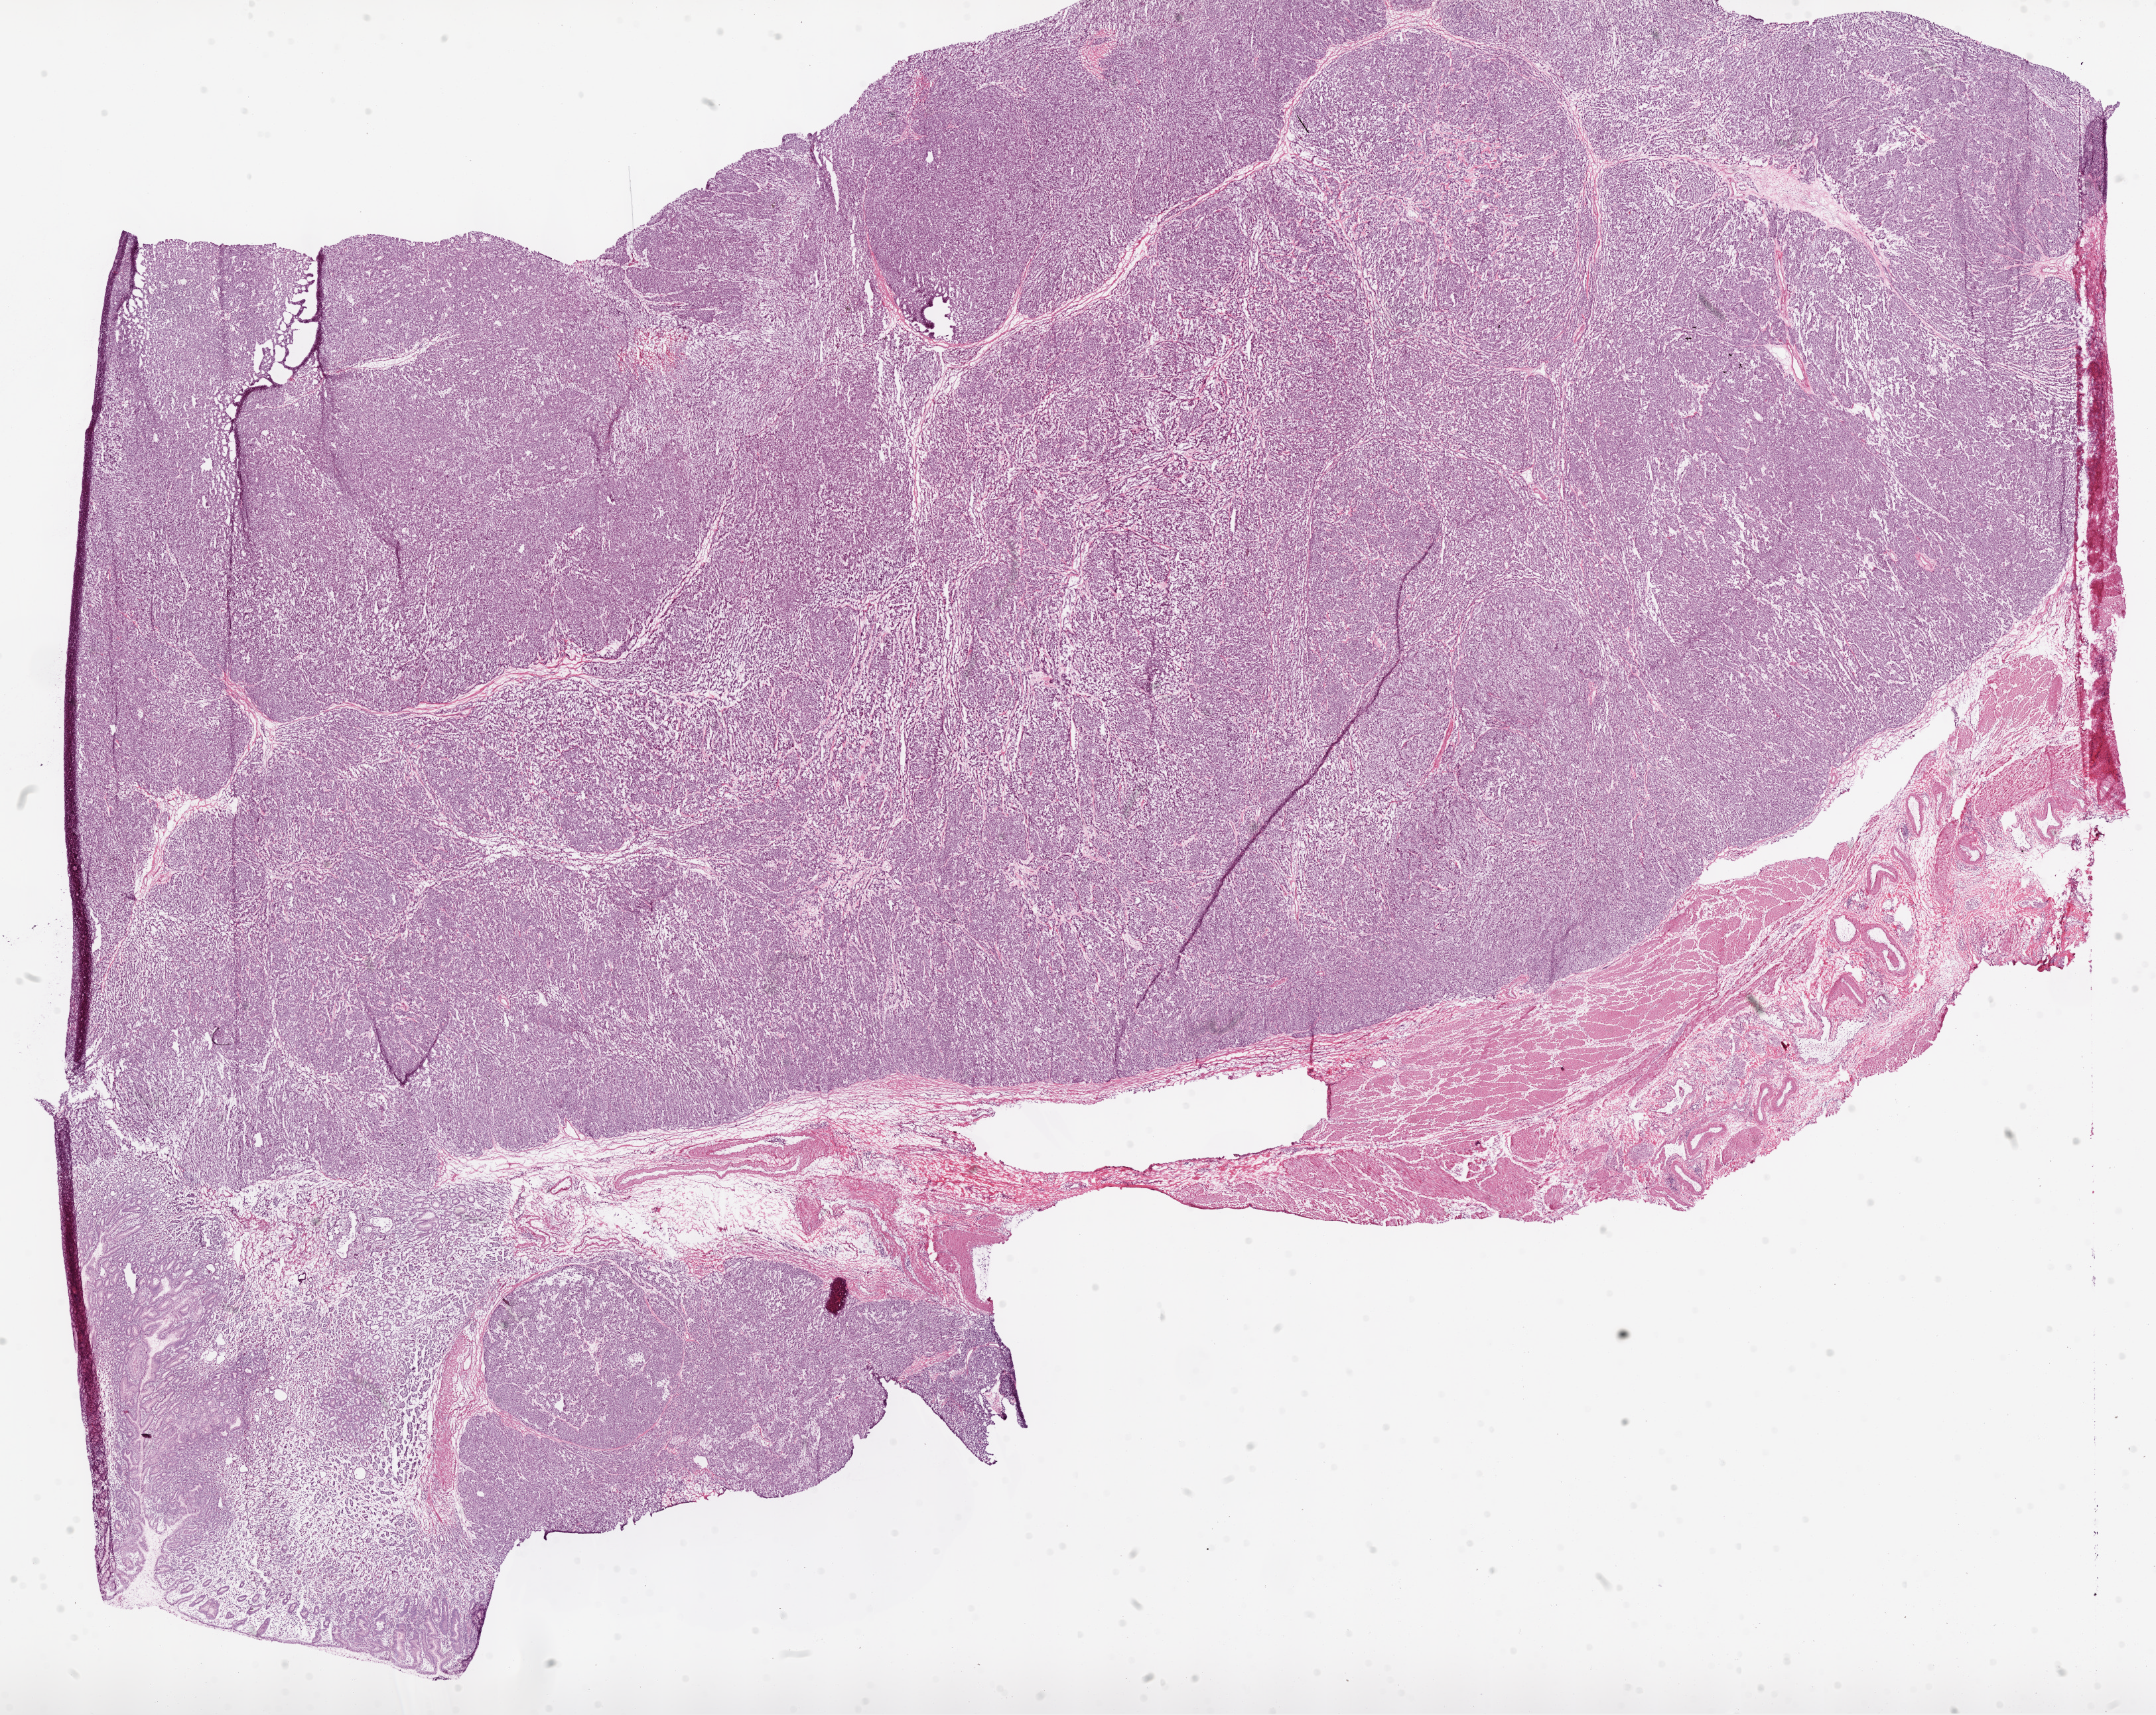
Whole-slide histology image, Hematoxylin and eosin (H&E) stained — a low-resolution overview of the entire scanned area, about 26.1 x 20.7 mm (acquisition: 20x scan). Frozen section from the bottom of the tissue portion. Primary tumour sample from the stomach. Patient: male, age at initial diagnosis 65 years. Histologic grade: G2 (moderately differentiated). Pathologist review of this section (percent, as recorded): tumour cells 86%, tumour nuclei 85%, normal cells 8%, stromal cells 5%, necrosis 1%.
Pathologic diagnosis: Tubular adenocarcinoma (body of stomach).